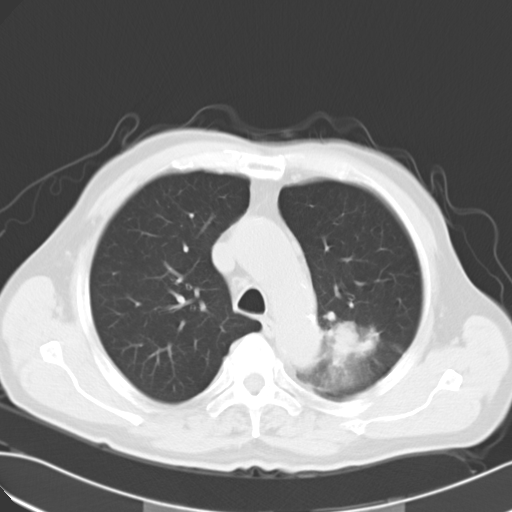
Chest CT, one axial slice. Slice 21 of 28 in the series (ordered by position). Reconstruction kernel B40f. 120 kVp. Lung window (W 1500 / L -600 HU). 10 mm slice thickness. 512 × 512 image matrix. Patient: male, 63 years. Case-level facts recorded for this patient, not image findings: clinical TNM (as recorded): T3 N3 M1a.
Outlined on this slice (rectangle marked by the reading radiologist):
- lung tumour (recorded histology: large cell carcinoma): bounding box (x1, y1, x2, y2) in pixels: (325, 313, 378, 372)